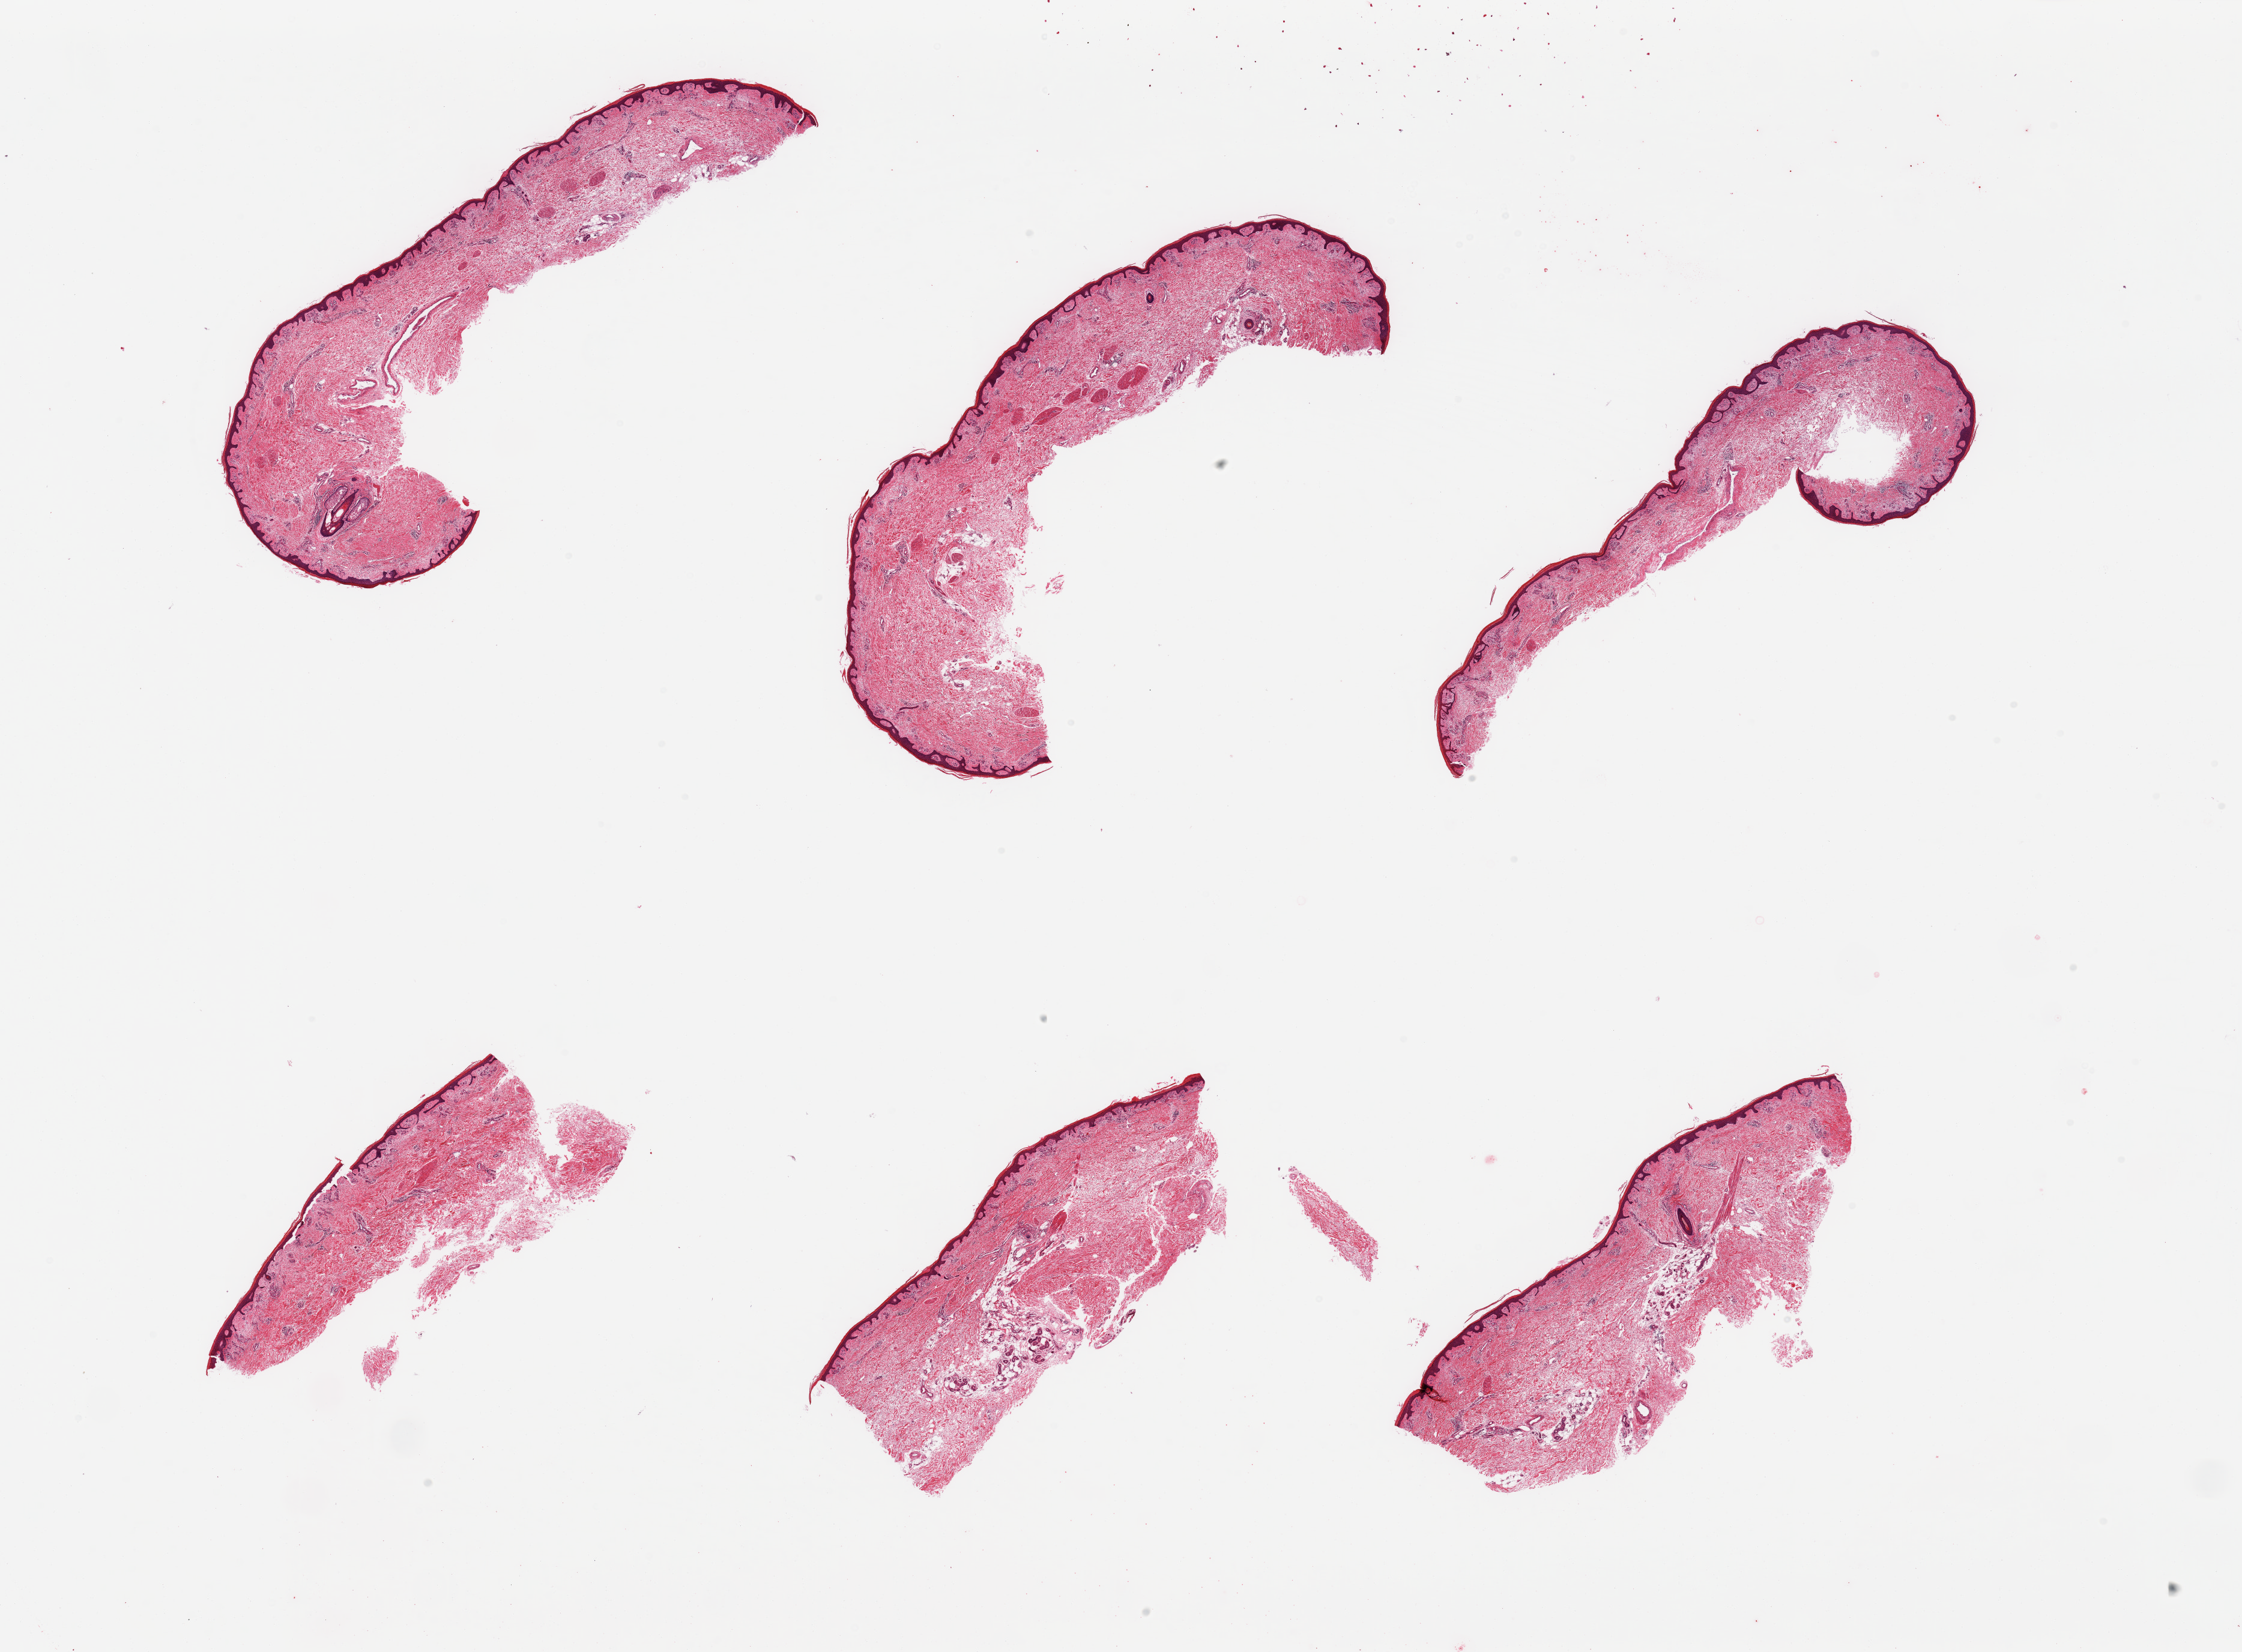
Digitized haematoxylin and eosin-stained section, brightfield, whole scanned area (about 29.5 x 21.8 mm) shown as a low-resolution overview, PAXgene-fixed, paraffin-embedded tissue, target tissue: skin of lower leg, donor tissue sample. Donor sex: male.
Review note (as recorded): 6 pieces, minimal dermal fat; squamous epithelium up to ~30 microns.